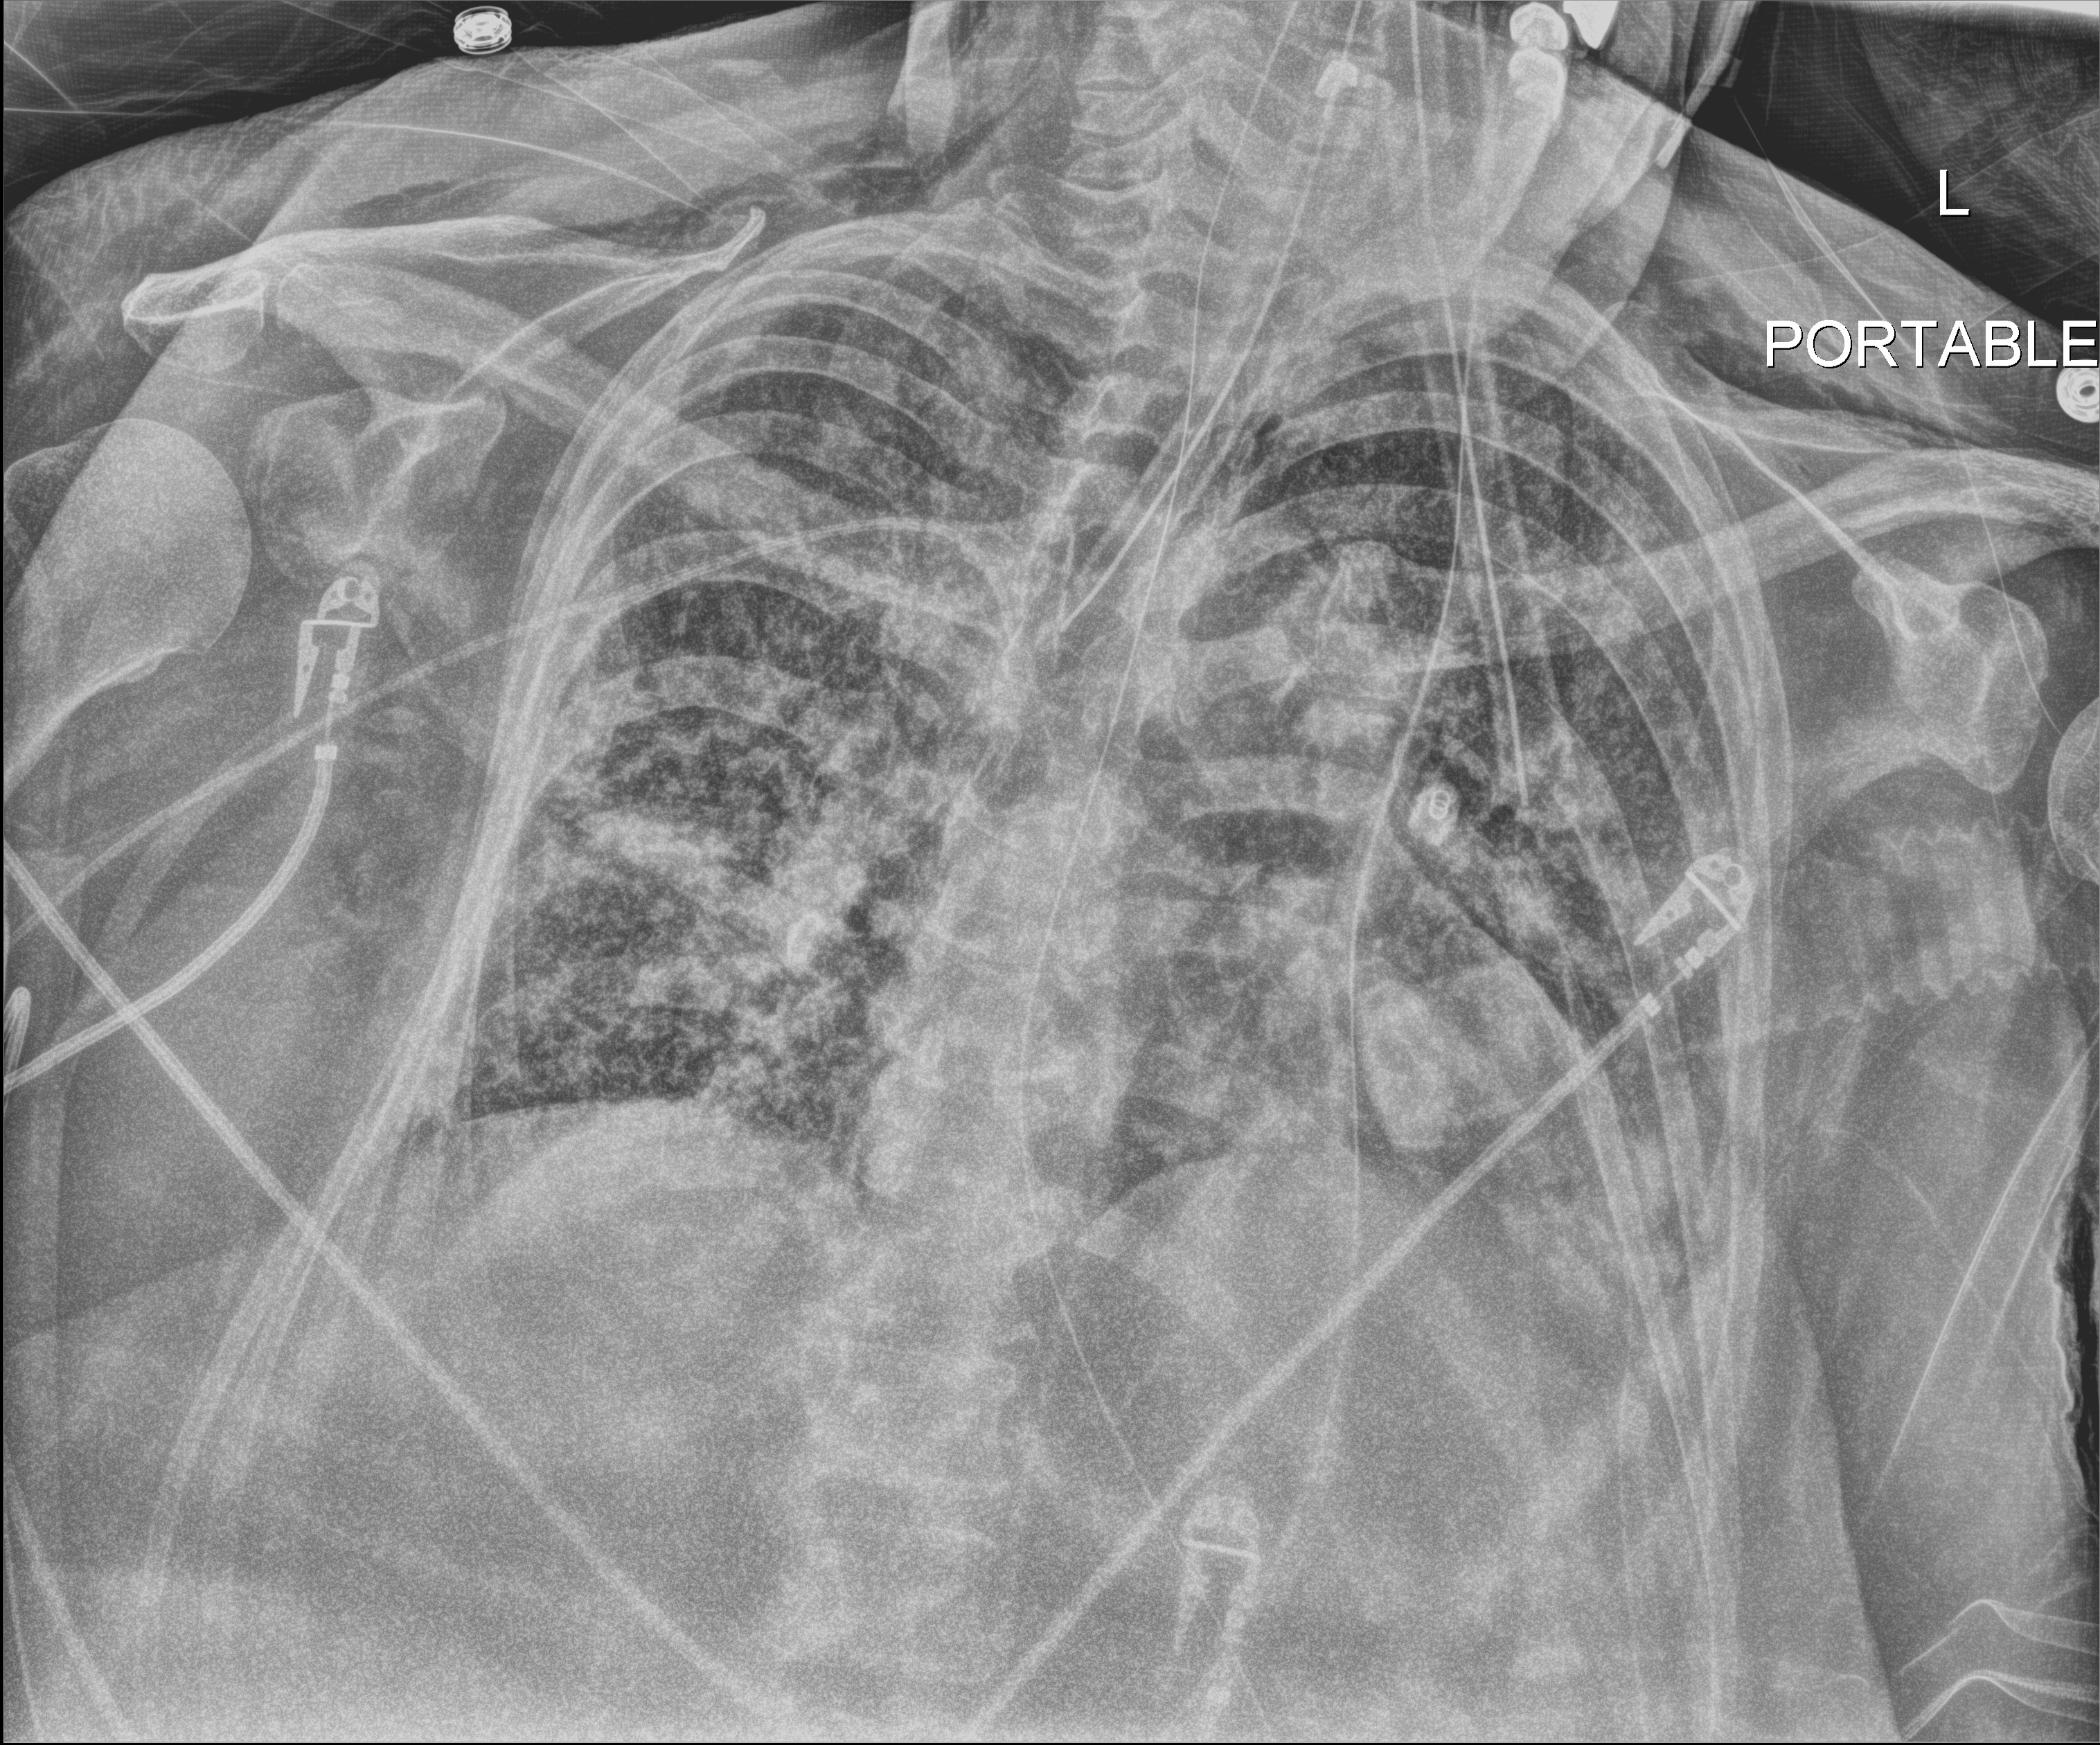
Portable chest radiograph; anteroposterior (AP) projection. Patient hospitalised with COVID-19; female, aged 60–74 years.
Admission-level facts for this patient (not findings on this image; timing relative to this image not recorded): COPD (admission record): no; admitted to intensive care during this hospital stay: yes.